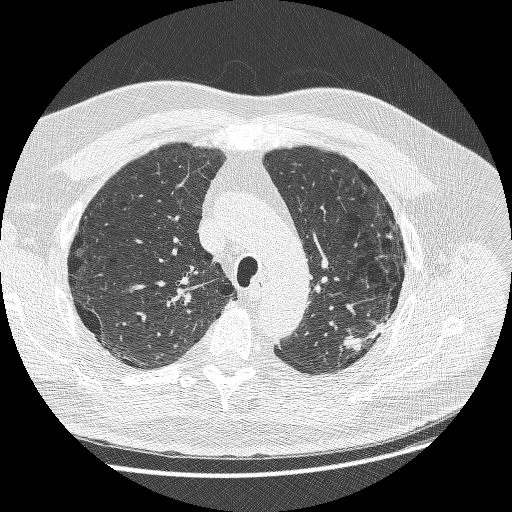
Axial slice from a low-dose chest CT screening exam. Baseline screening round. Lung window (W 1500 / L -600 HU). Lung (sharp) reconstruction kernel (BONE). Male participant, aged 68 years at enrolment.
- Expert reader's lesion annotation, bounding box [x1, y1, x2, y2] px = [335, 310, 391, 362].
- The exam's reader record, not a measurement of the box and not confirmed to be the same lesion: non-calcified nodule or mass ≥4 mm, left upper lobe, 15 × 14 mm, smooth margins, soft tissue attenuation.
- Participant outcome: lung cancer diagnosed 19 days after this screen — adenosquamous carcinoma, left upper lobe, poorly differentiated (G3), stage IIIB (AJCC 6th edition), 32 mm at pathology.